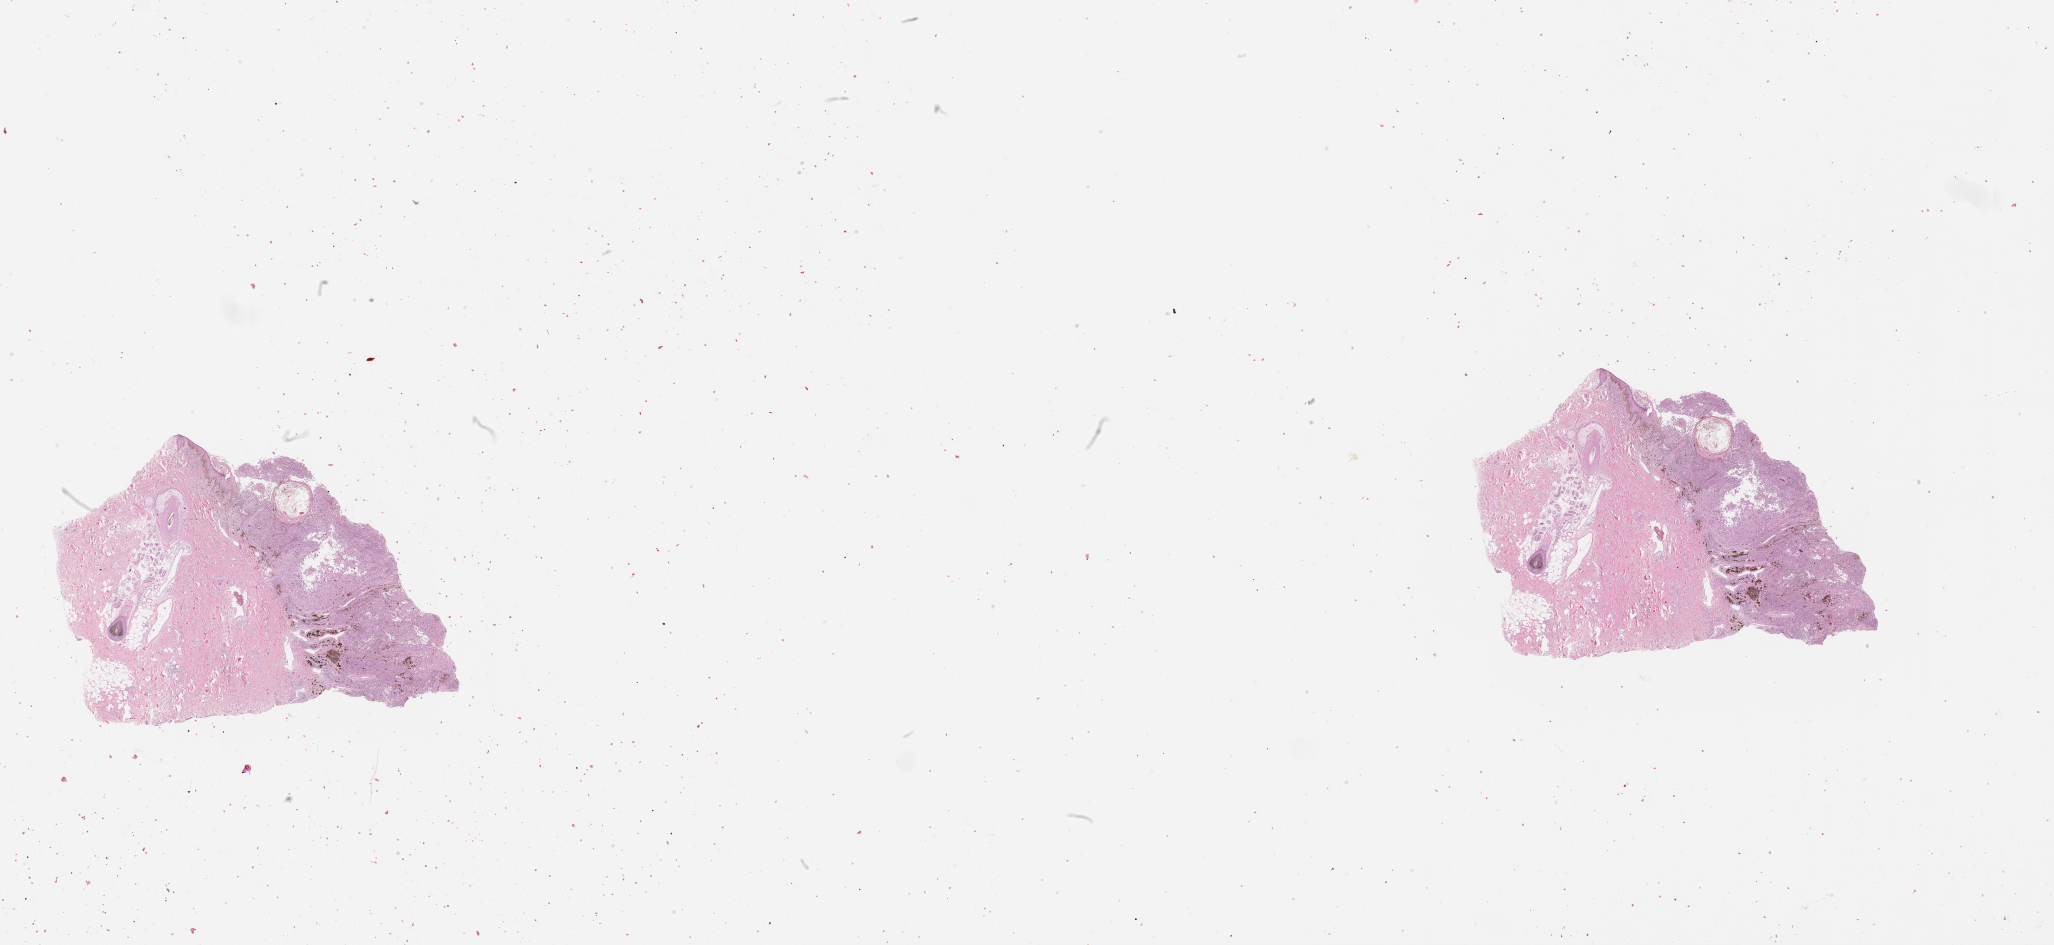
Hematoxylin and eosin (H&E) stained whole-slide image — shown as a low-resolution overview of the whole scanned area (about 33.1 x 15.2 mm). Patient: male, age 61 years.
Patient diagnosis: Malignant melanoma, NOS.